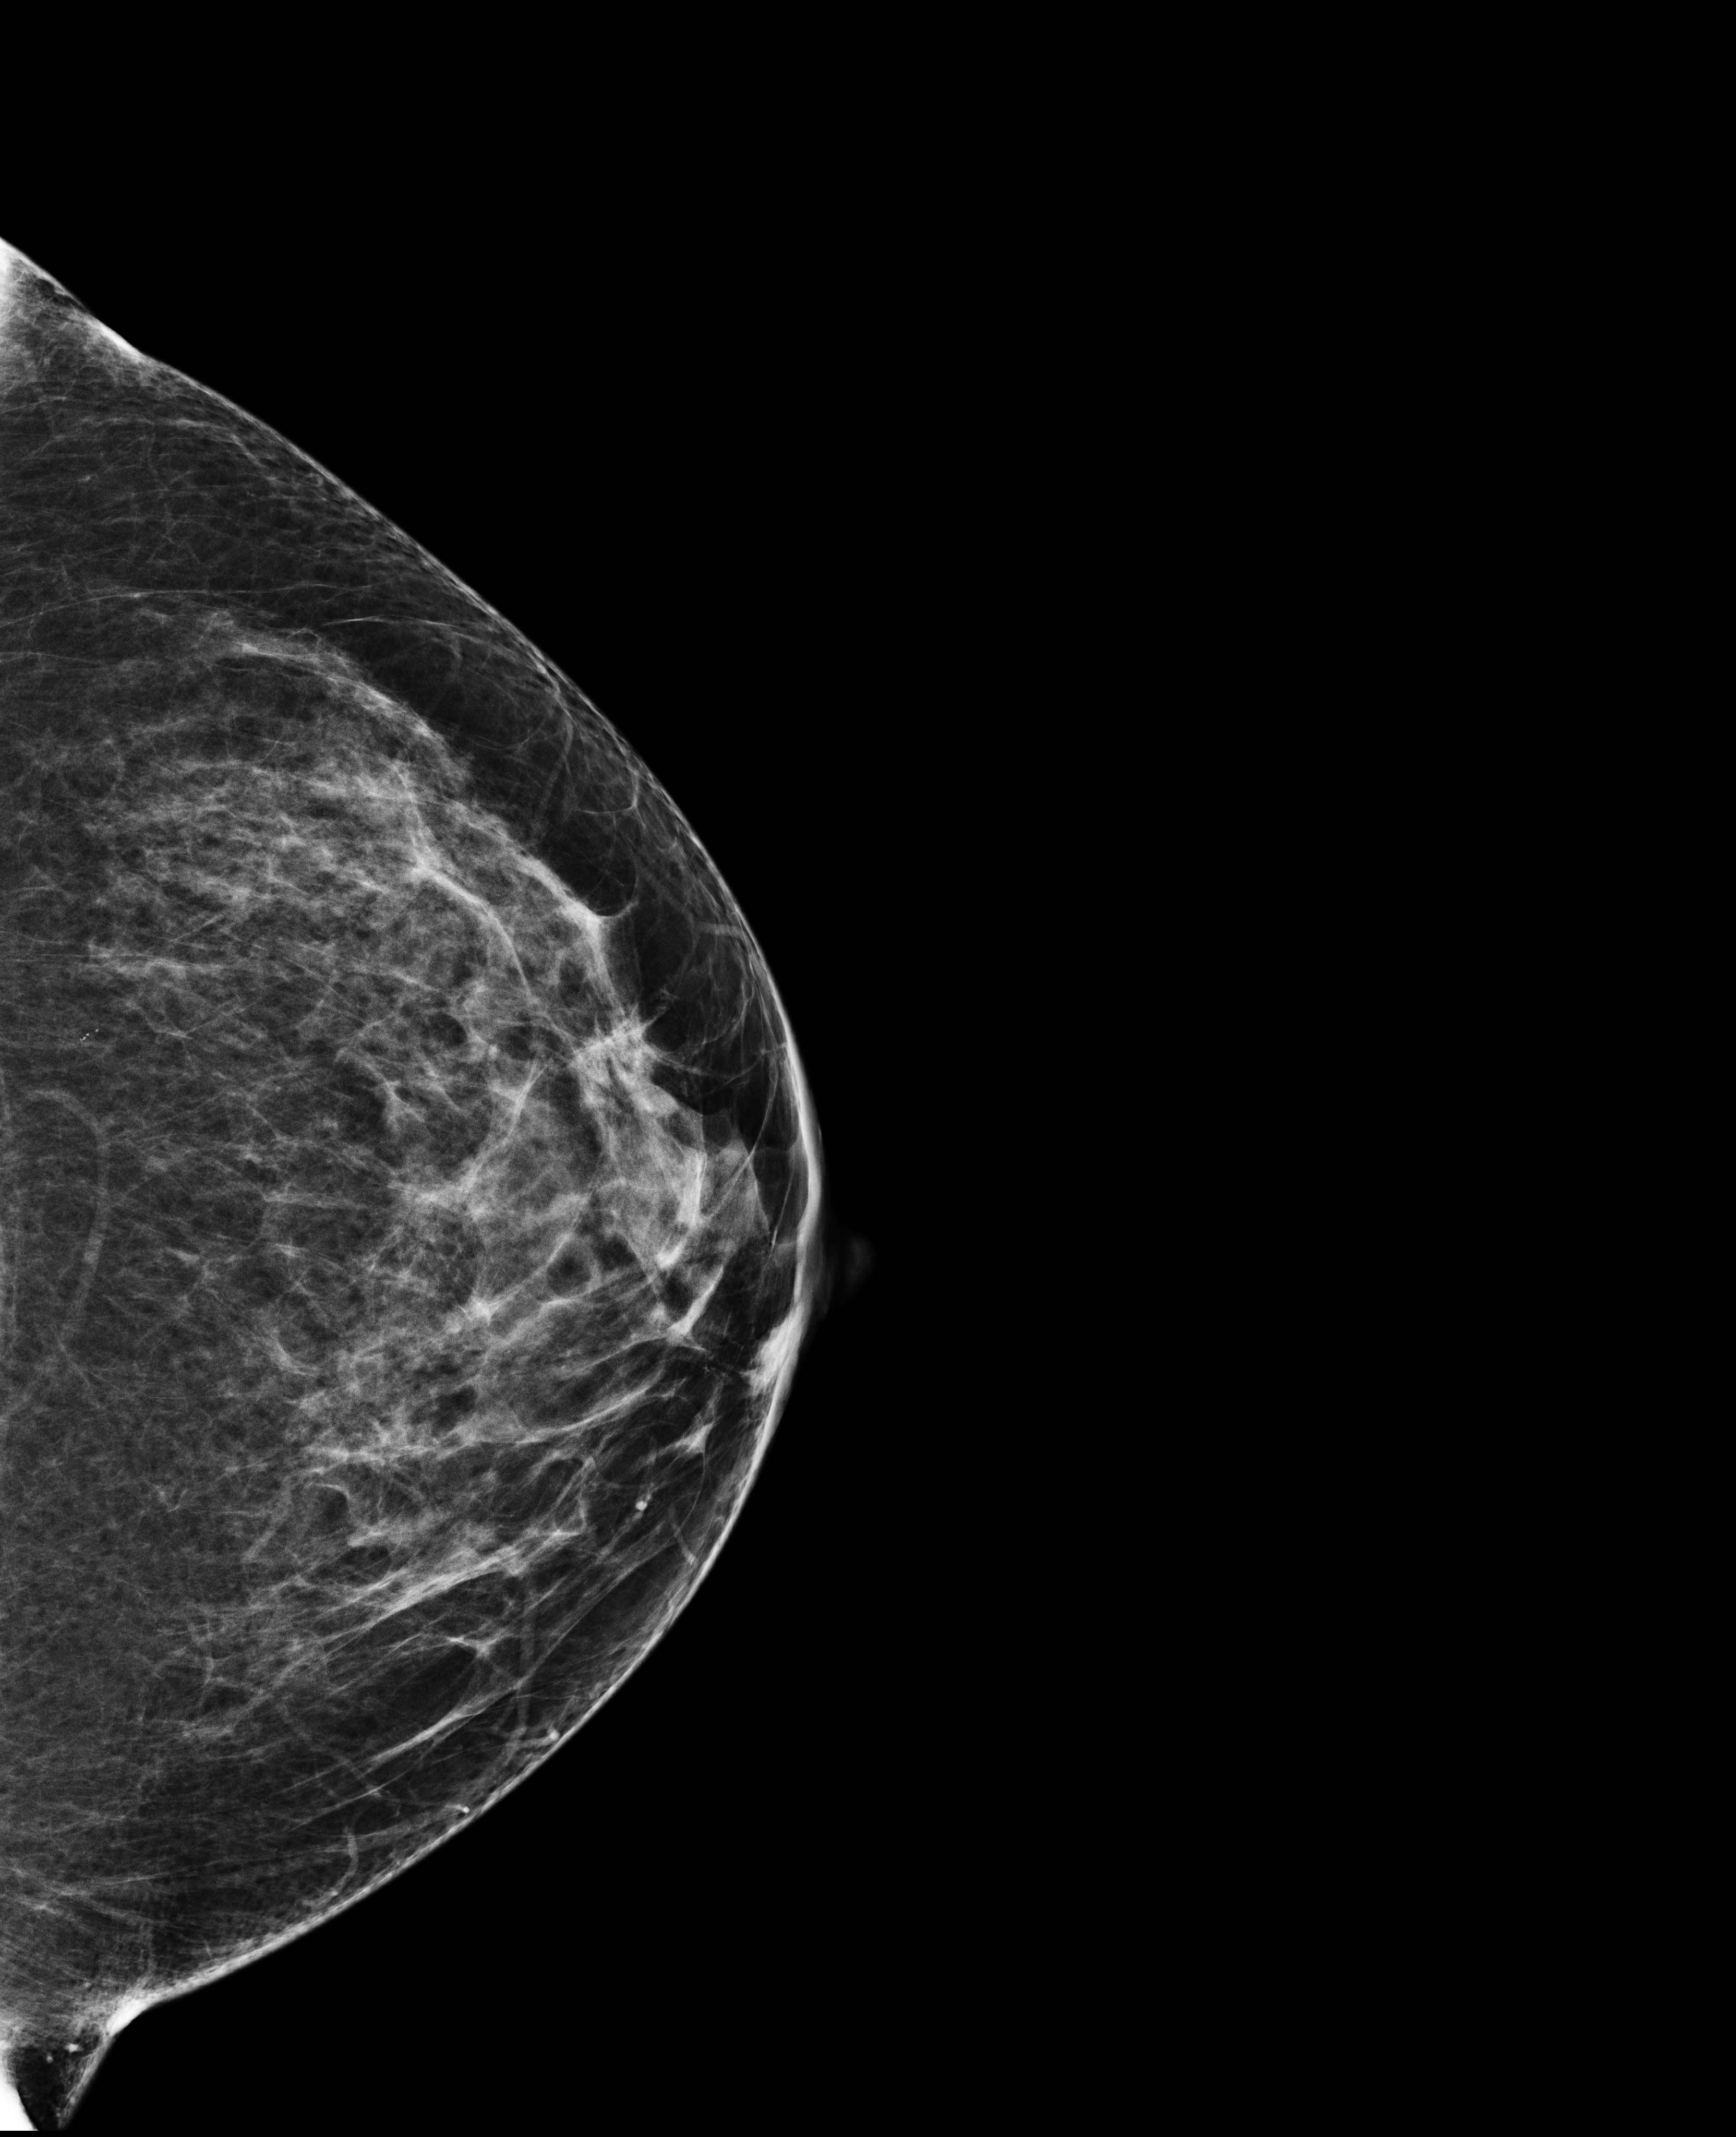
Screening examination; compressed breast thickness 61 mm; system: Selenia Dimensions. Patient aged 56 years (female).
Image type: full-field digital mammogram. Breast: left. Projection: craniocaudal (CC) view. BI-RADS breast density category at the screening exam (both breasts, scale 1–4): 3. Final BI-RADS category for the screening round (tomosynthesis exam, both breasts): category 1. Recall: recalled for additional imaging after this screen.